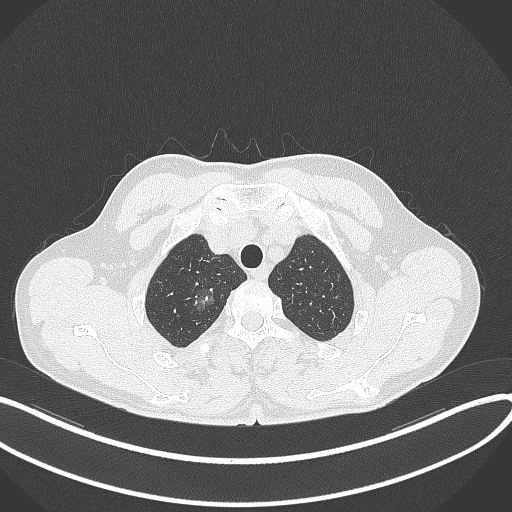
Chest CT, one axial slice; 120 kVp; lung window (W 1500 / L -600 HU); 1 mm slice thickness; 512 × 512 image matrix. Patient: male, 58 years. From the clinical record (not read from this slice): clinical TNM (as recorded): T1c N0 M0.
Annotated regions visible in this slice (rectangle marked by the reading radiologist):
- lung tumour (recorded histology: adenocarcinoma): bounding box (x1, y1, x2, y2) in pixels: (183, 282, 223, 317)